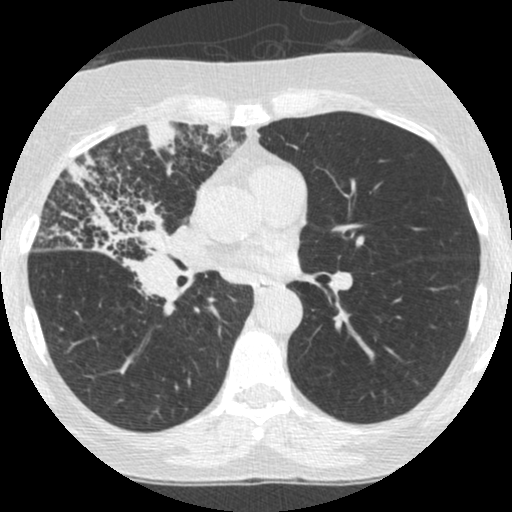
Low-dose screening chest CT, one axial slice. Slice 140 of 253 in the series (ordered by position). 120 kVp. Lung window (W 1500 / L -600 HU). 512 × 512 image matrix.
Annotated regions visible in this slice (outlined manually by an expert reader):
- lesion 2 (tumor, hilum of right lung): bounding box [x1, y1, x2, y2] px = [40, 161, 191, 270]
- lesion 3 (tumor, upper lobe of right lung): [144, 121, 178, 157]
- lesion 4 (tumor, upper lobe of right lung): [203, 125, 239, 159]